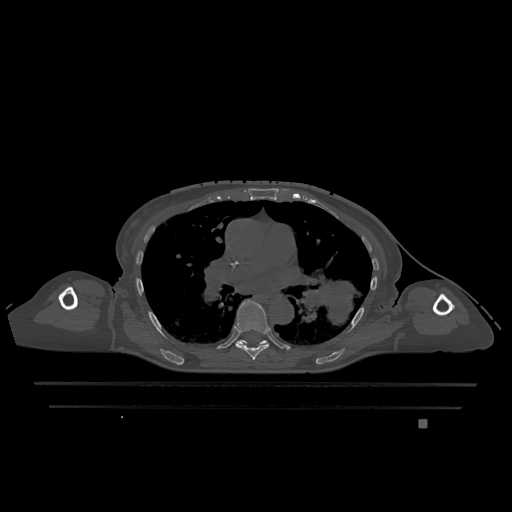
CT including the spine, one axial slice; position 775 of 1317 along the scan axis; bone window (W 1800 / L 400 HU); 0.5 mm slice thickness; 512 × 512 image matrix, field of view 500 × 500 mm. Female patient, age 74 years. From the clinical record (not read from this slice): primary cancer: lung.
Annotated regions visible in this slice (semi-automatic segmentation, software-assisted and operator-edited):
- T6 vertebra: box from (x=235, y=300) to (x=270, y=360) px
- T7 vertebra: (x=237, y=340)–(x=268, y=345)